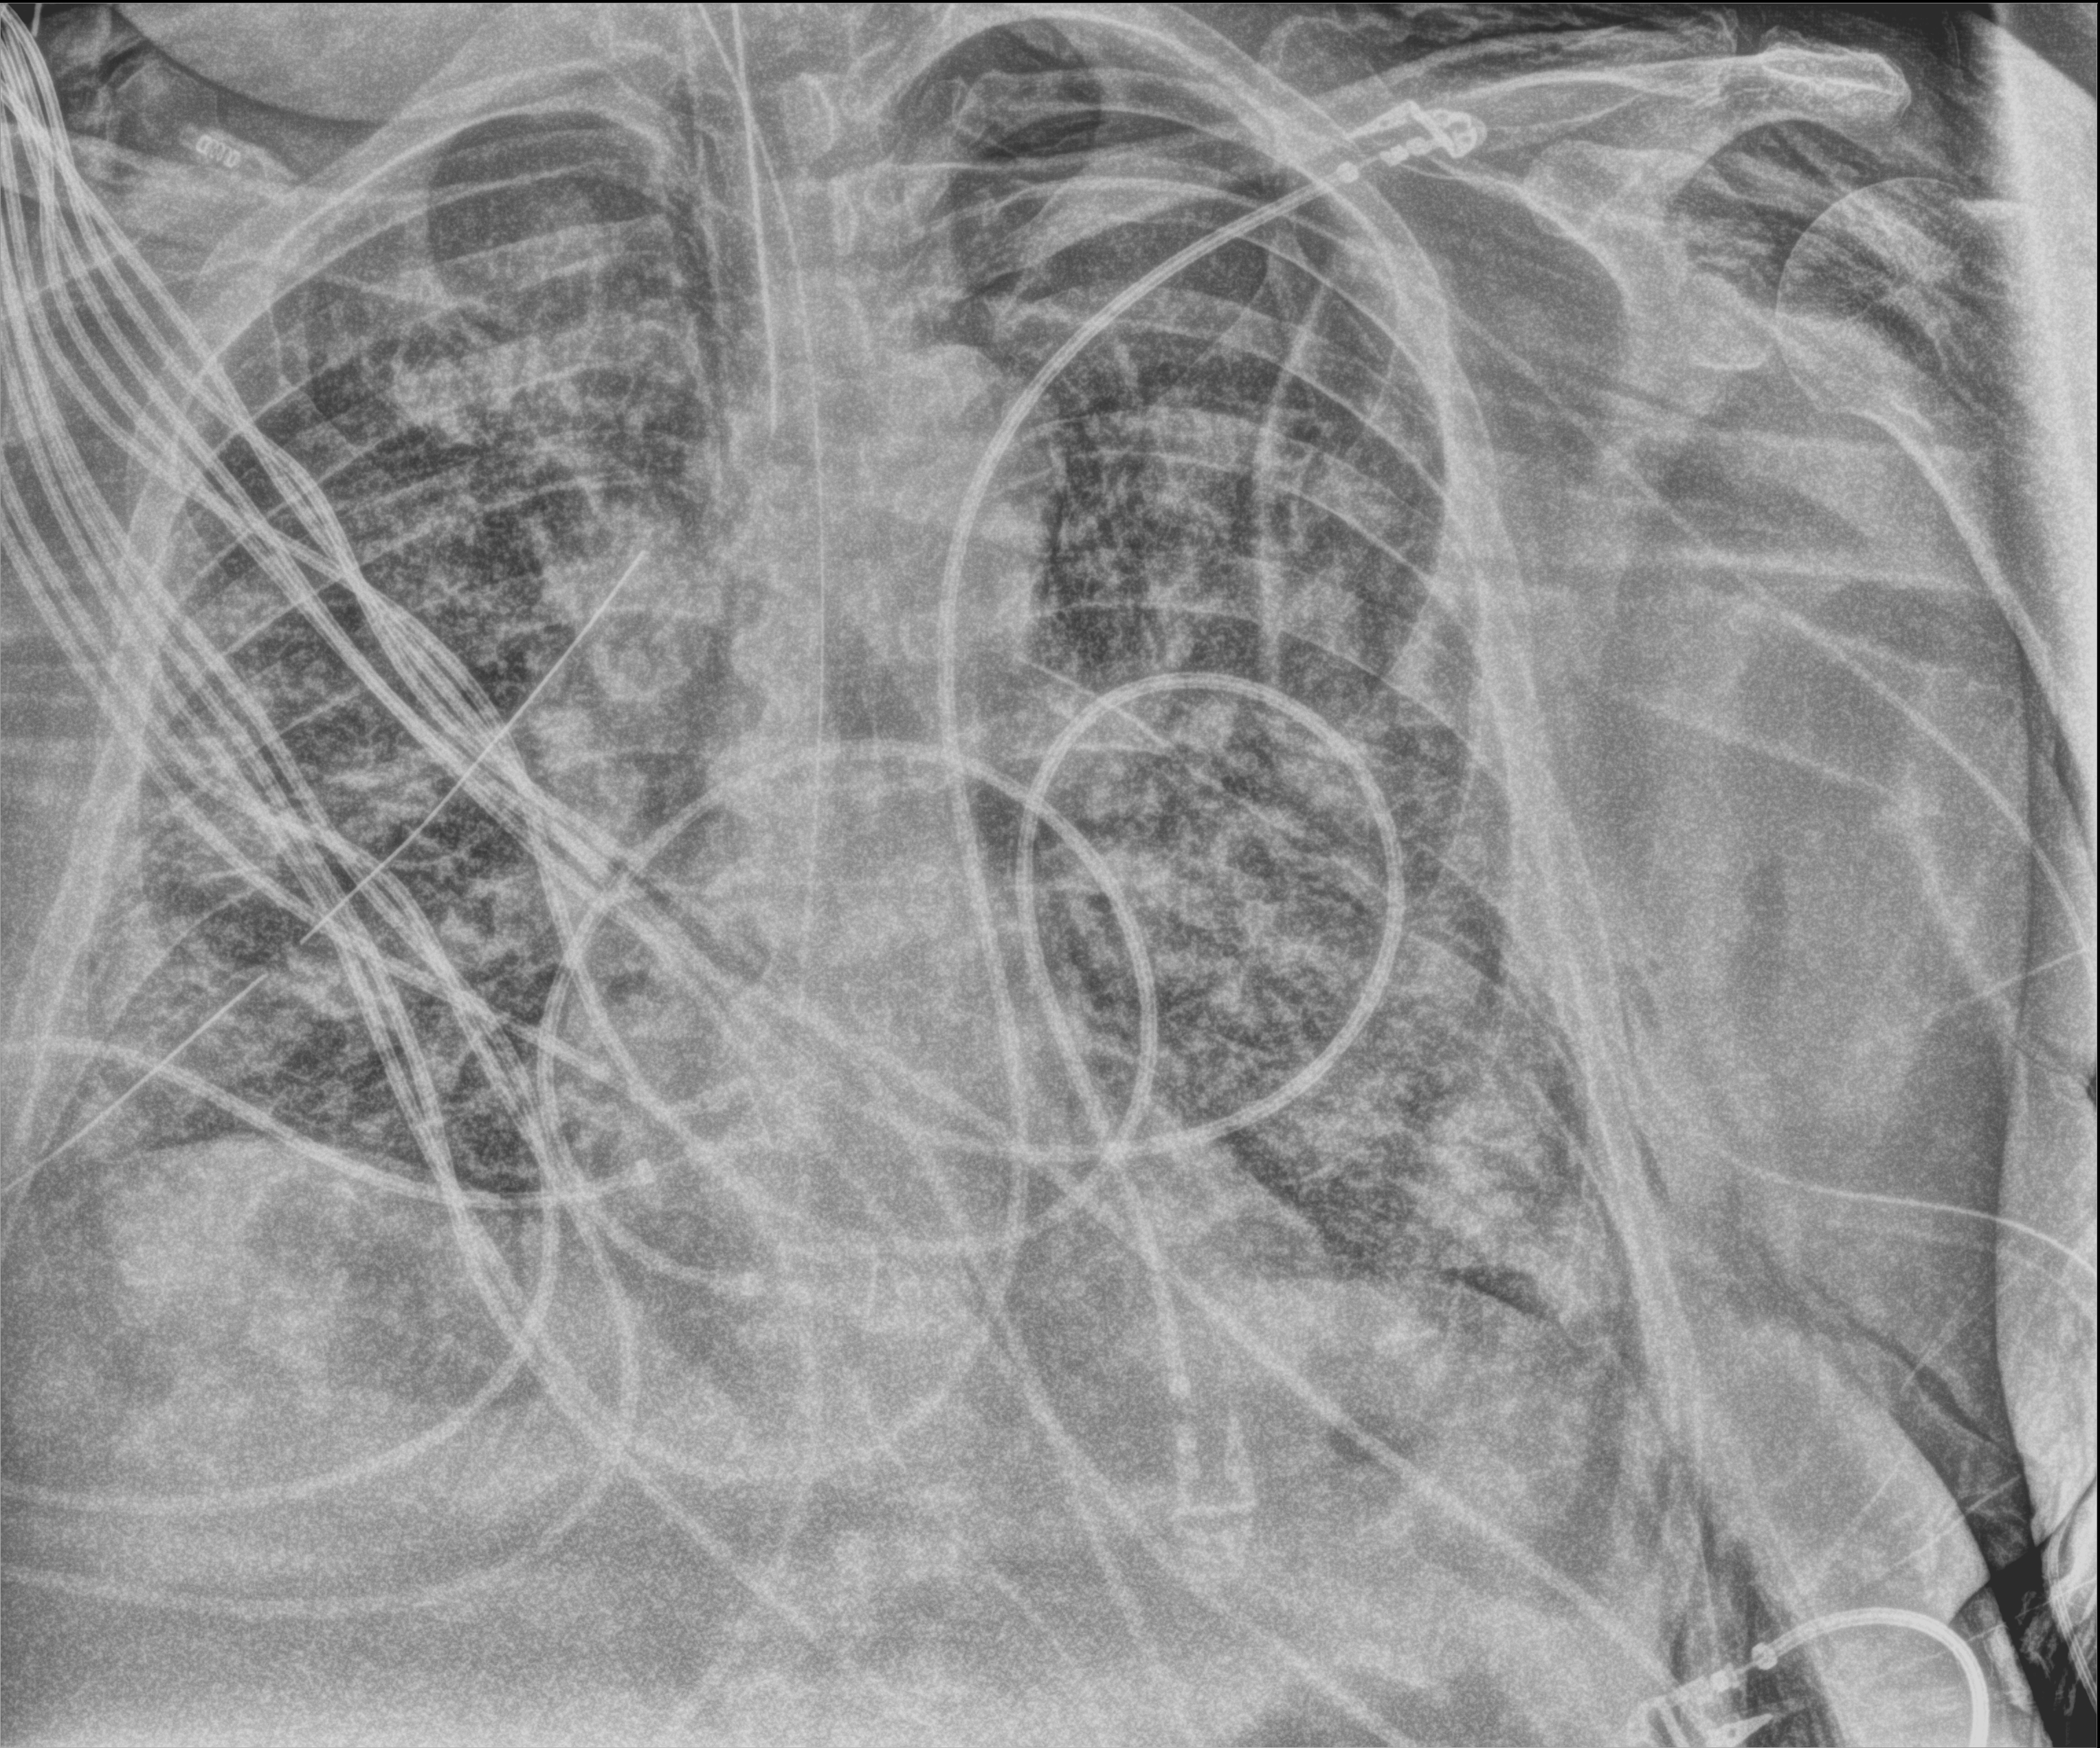
Bedside chest radiograph (computed radiography). Adult patient hospitalised with COVID-19, age 18–59 years.
Hospital-stay facts (about this admission, not read from this image; timing relative to this image not recorded): length of hospital stay: 28 days; admitted to intensive care during this hospital stay: yes.